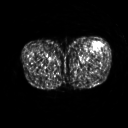
FDG PET of an extremity soft-tissue mass (from a PET/CT study), one axial slice. Slice 219 of 267 in the series (ordered by position). 3.27 mm slice thickness. 128 × 128 image matrix, field of view 500 × 500 mm. Male patient, age 64 years. From the clinical record (not read from this slice): histological type: extraskeletal osteosarcoma; grade: high; site of the primary tumour: thigh.
Structures marked on this image (expert contour drawn on MRI and transferred to this co-registered scan by the dataset authors):
- gross tumour volume (mass): bounding box [x1, y1, x2, y2] px = [94, 43, 100, 51]